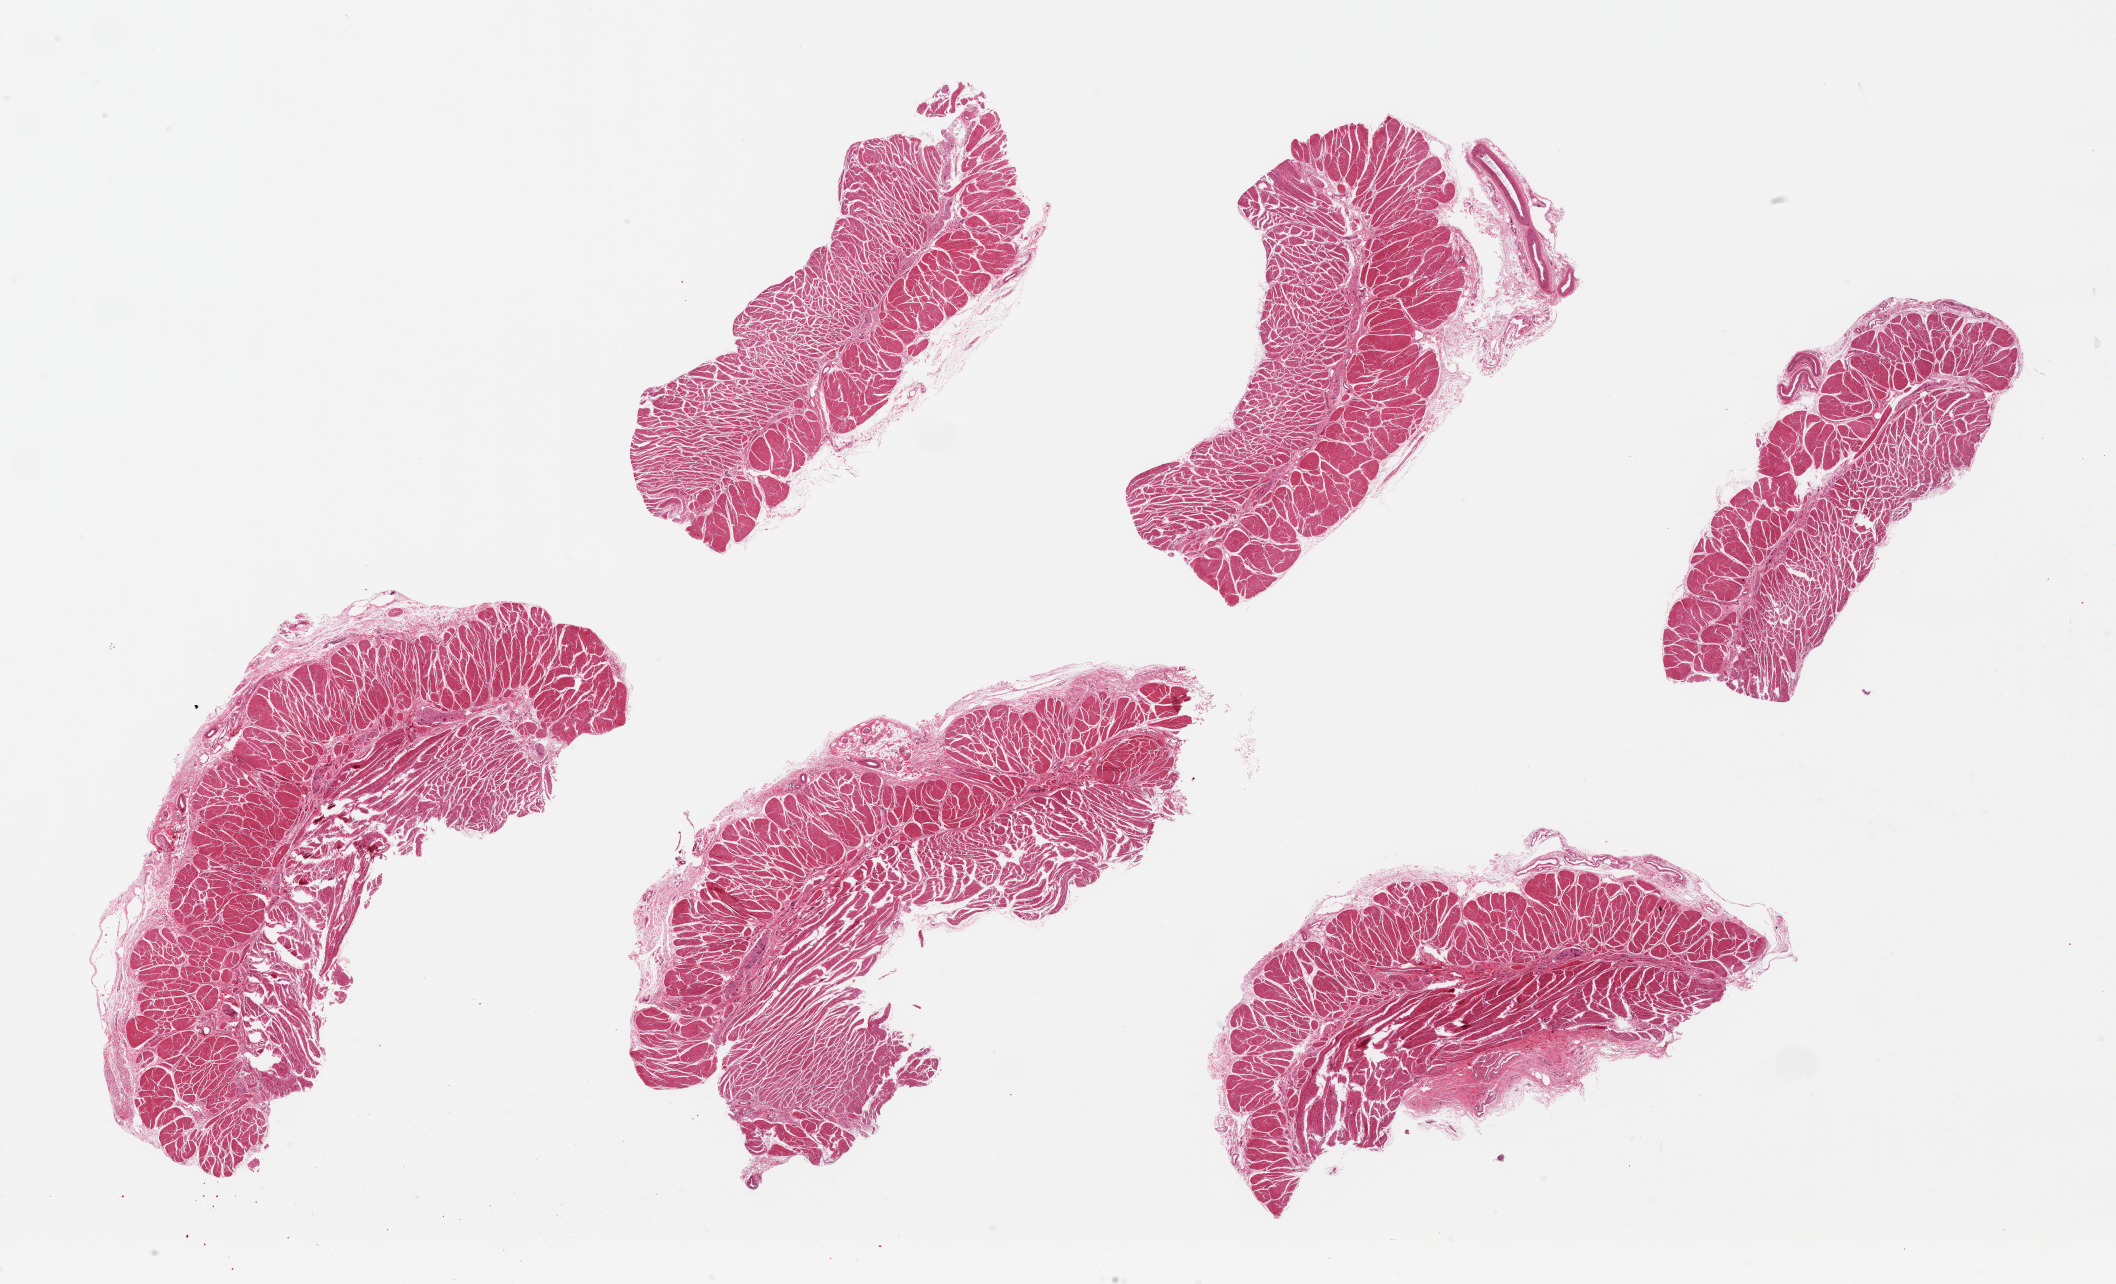
Whole-slide image, haematoxylin and eosin stain, low-resolution overview of the scanned area, about 33.5 x 20.3 mm (slide scanned at 20x), PAXgene-fixed paraffin-embedded (PFPE) section, section of esophageal muscle (target tissue), tissue donor sample. Donor sex: male.
Review note (as recorded): 6 pieces ~8x3mm.